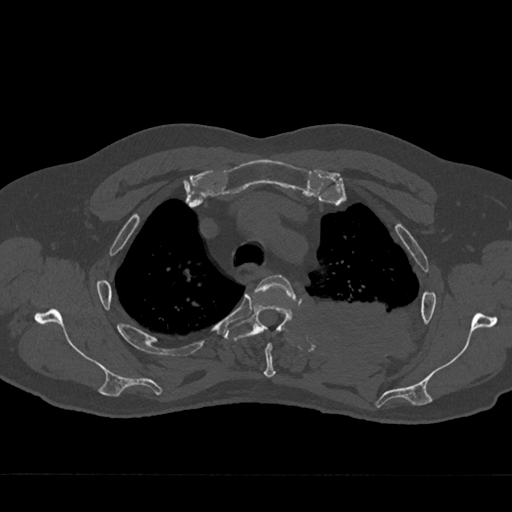
CT including the spine, one axial slice; slice 540 of 797 in the series (ordered by position); reconstruction kernel Br40s/3; 120 kVp; bone window (W 1800 / L 400 HU); 0.5 mm slice thickness; 512 × 512 image matrix, field of view 377 × 377 mm. Male patient, age 75 years. Case-level facts recorded for this patient, not image findings: primary cancer: renal.
Outlined on this slice (semi-automatic segmentation, software-assisted and operator-edited):
- T3 vertebra: bounding box (x1, y1, x2, y2) in pixels: (252, 275, 297, 378)
- T4 vertebra: (225, 304, 292, 341)